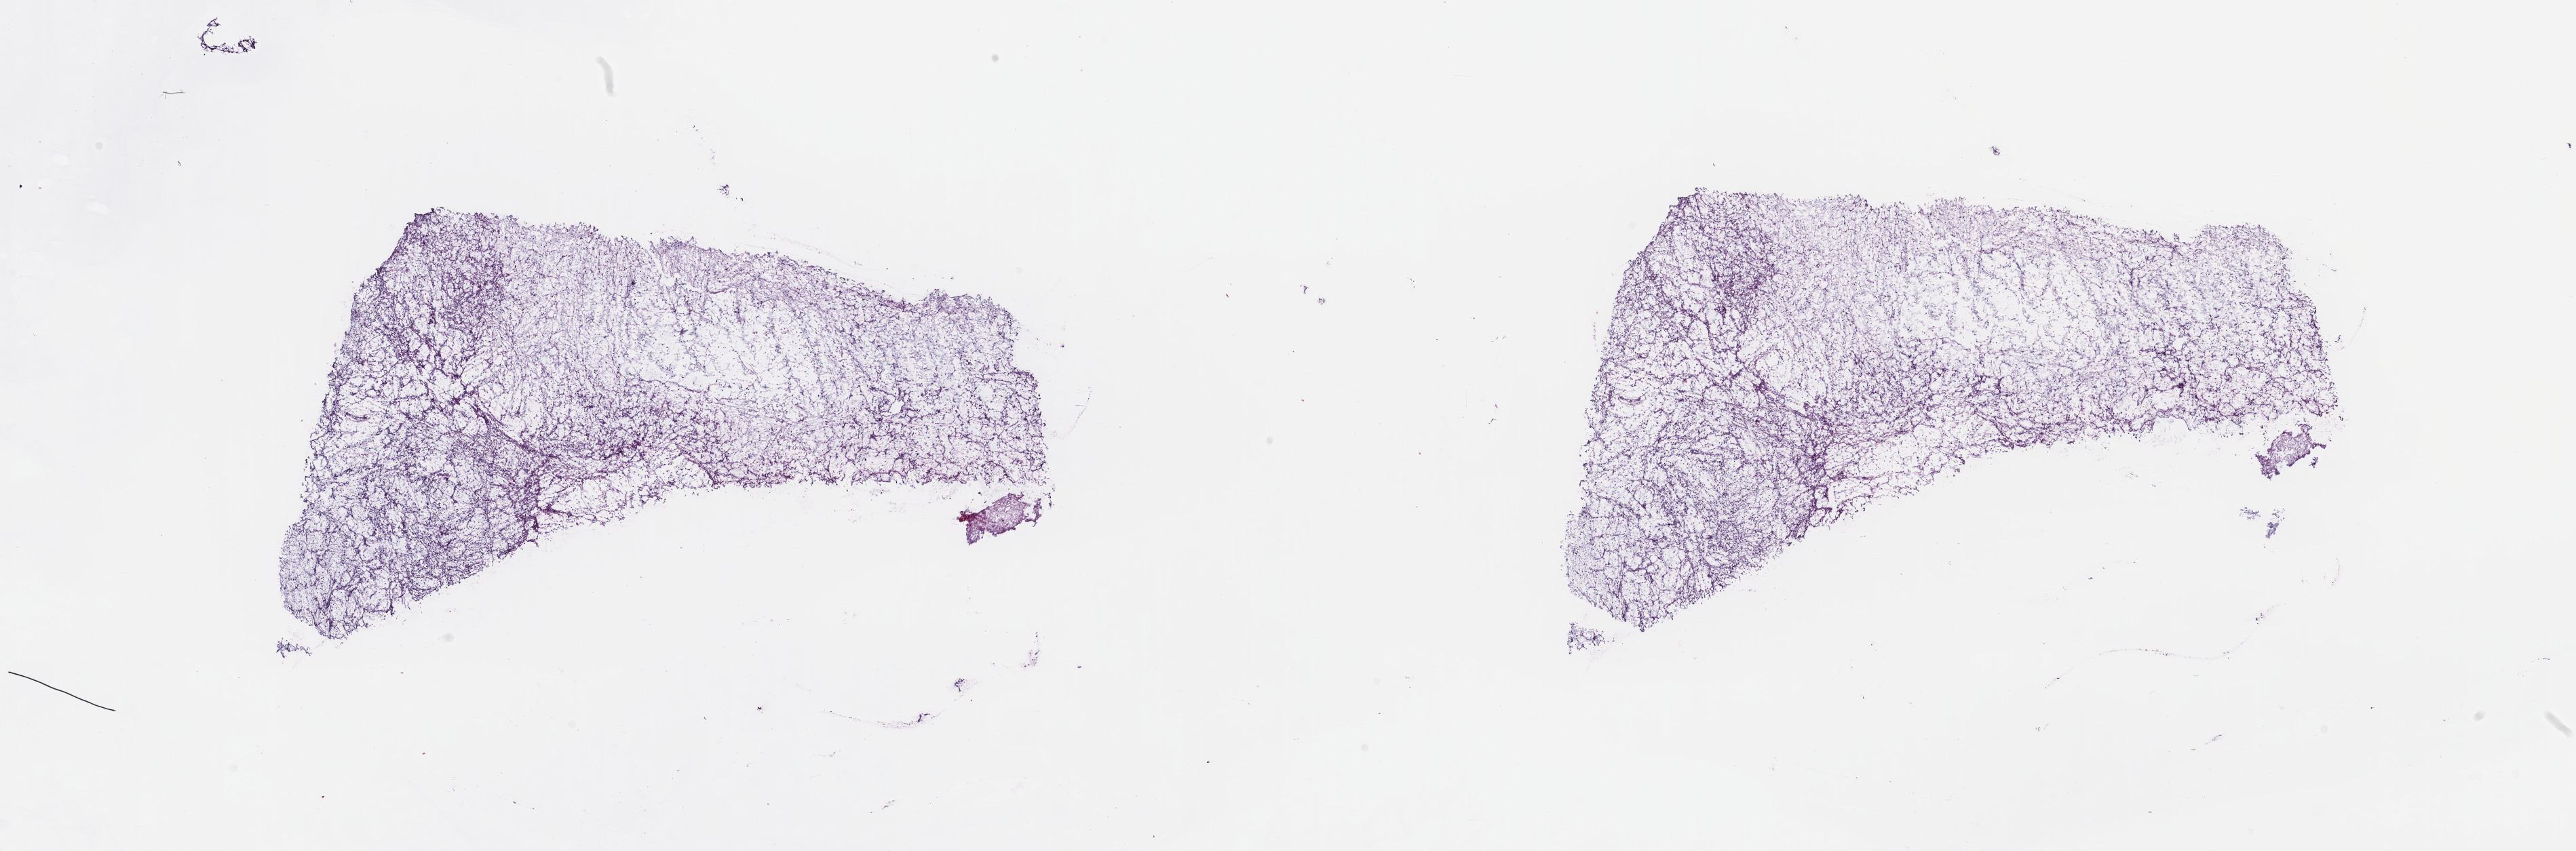
Whole-slide histology image, Hematoxylin and eosin (H&E) stained — a low-resolution overview of the entire scanned area, about 30.7 x 10.1 mm, frozen section from the top of the tissue portion, primary tumour sample from the retroperitoneum and peritoneum. Male, age 57 years at initial diagnosis. Composition of this section per pathologist review: tumour cells 100%, tumour nuclei 80%, normal cells 0%, stromal cells 0%, necrosis 0%. Inflammatory infiltration, as recorded: lymphocyte infiltration 2%, monocyte infiltration 0%, neutrophil infiltration 0%.
* diagnosis: Fibromyxosarcoma (retroperitoneum)